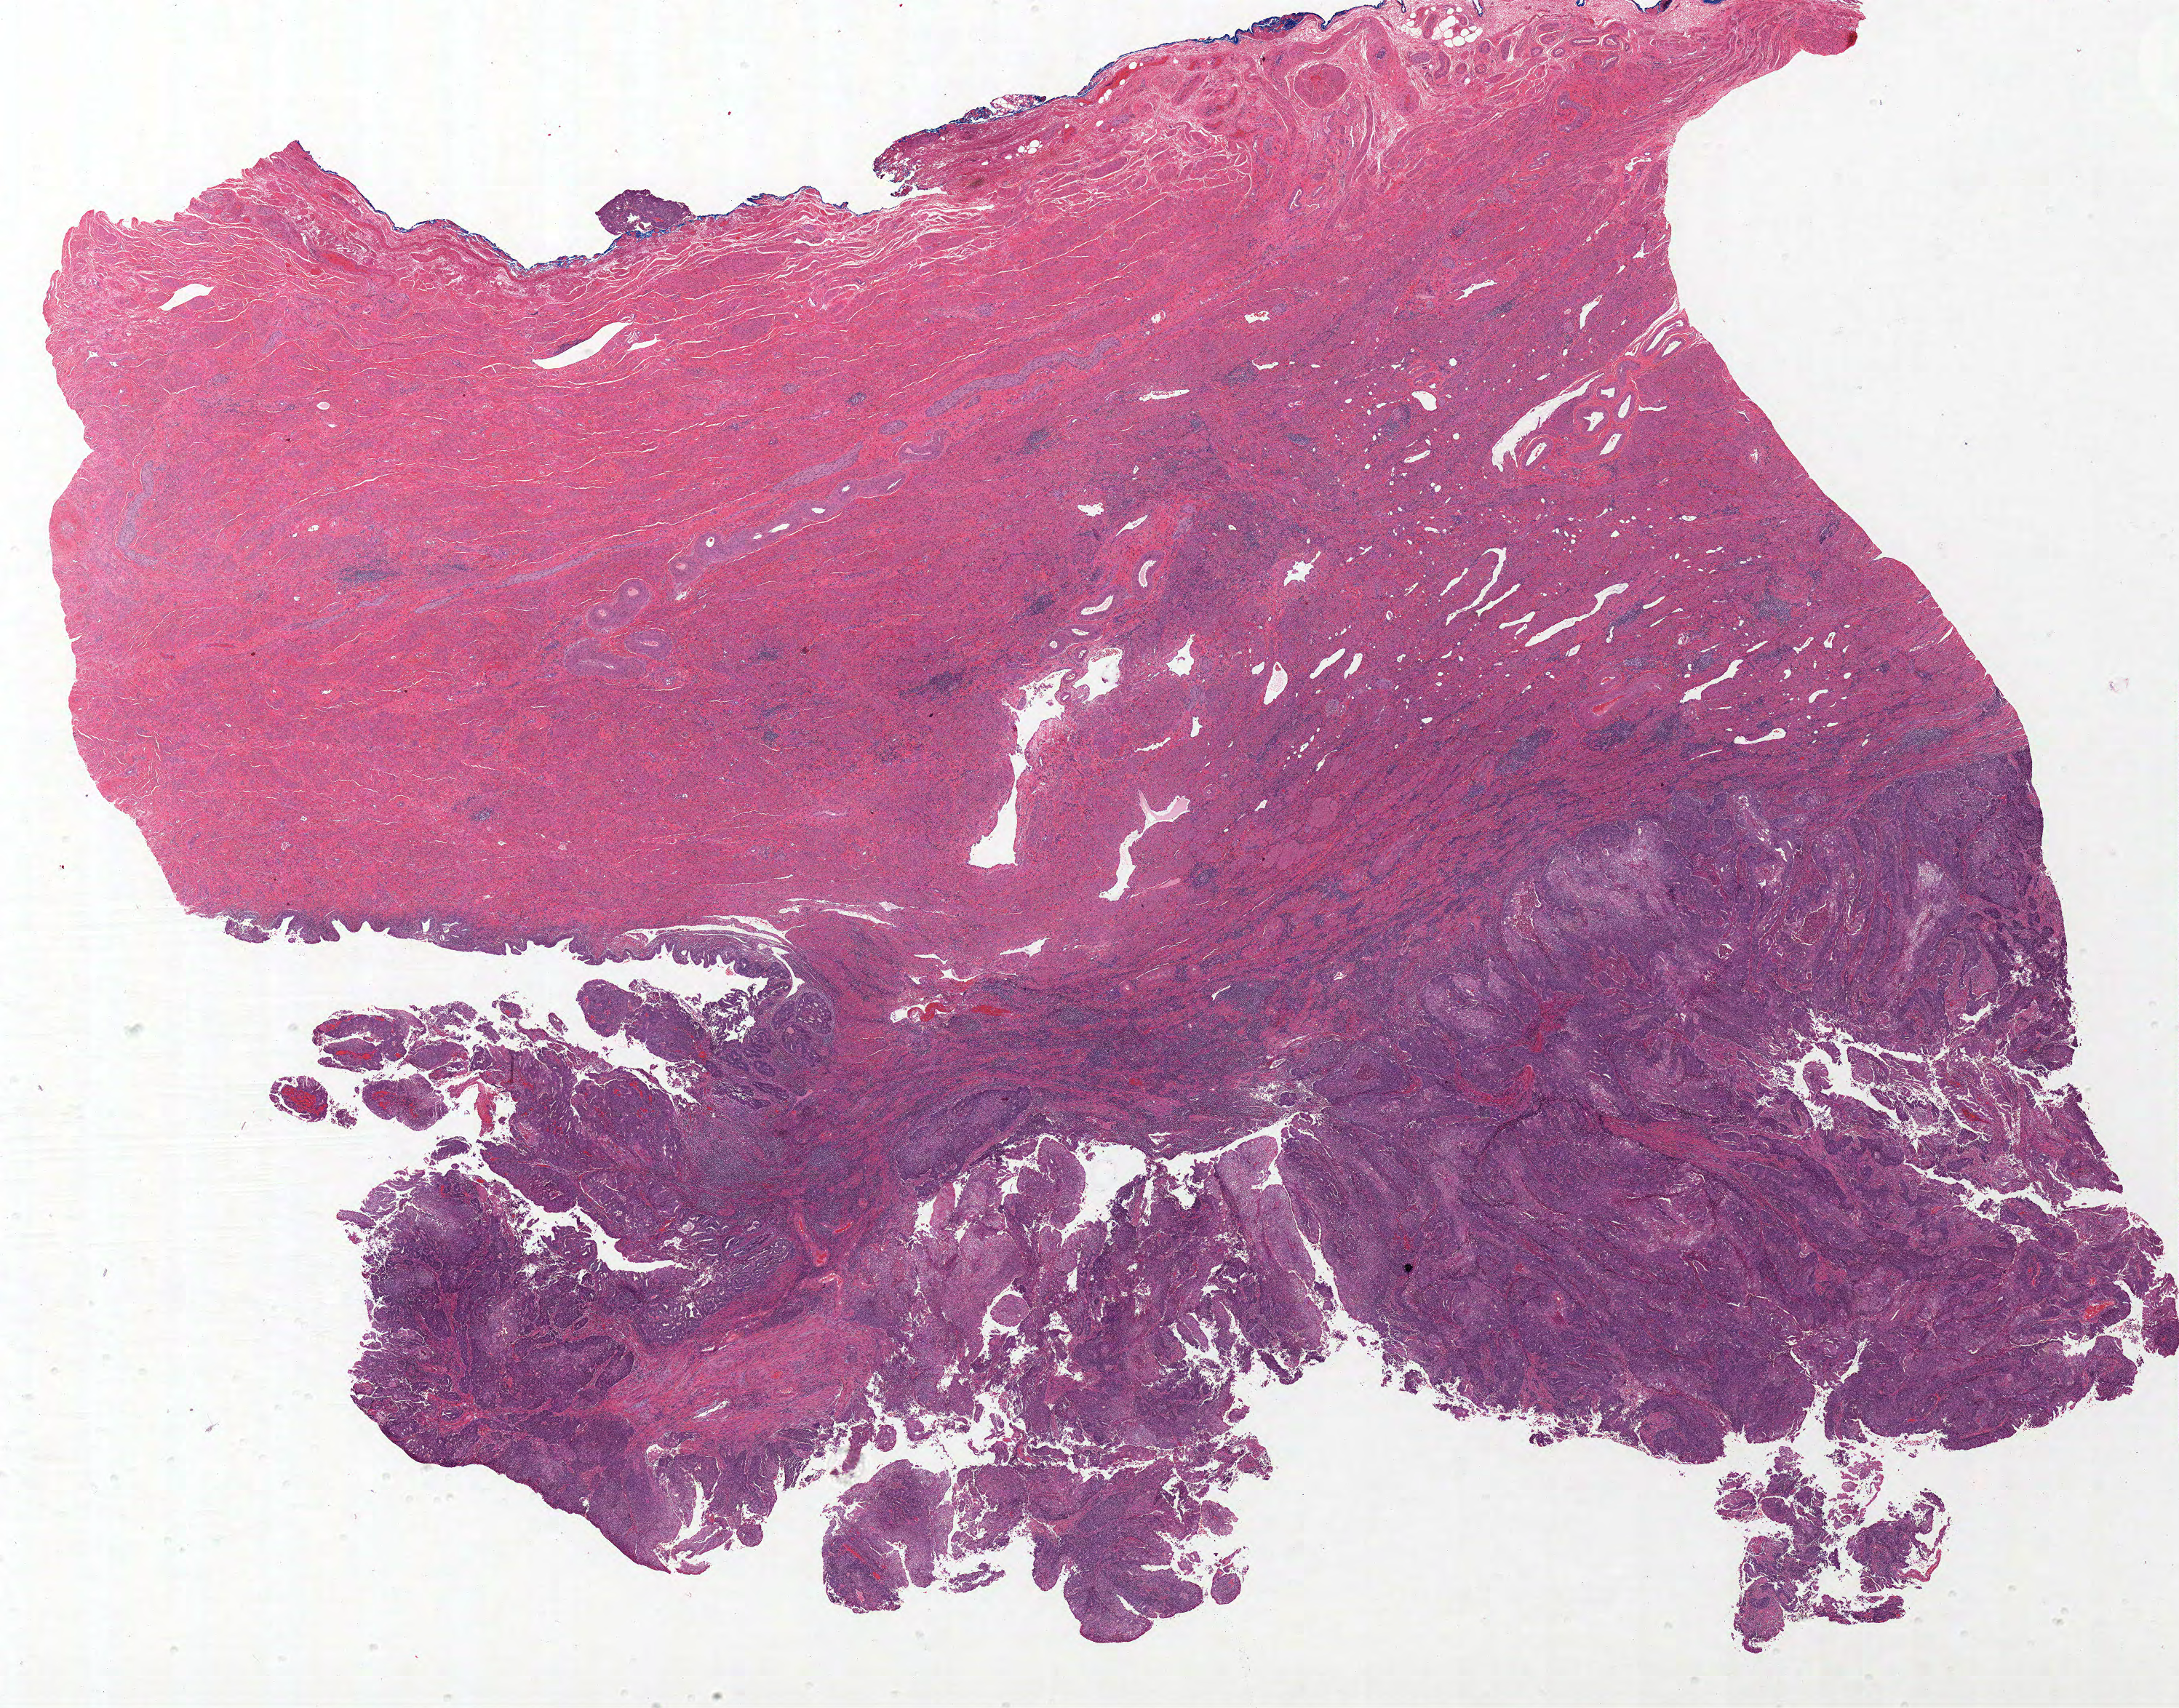
H&E whole-slide image, a low-resolution overview of the entire scanned area, about 23.9 x 18.7 mm (slide scanned at 20x), formalin-fixed paraffin-embedded (FFPE) diagnostic section, uterus, primary tumour sample. Patient: female, age at initial diagnosis 59 years. Histologic grade: G2 (moderately differentiated).
Diagnosis: Endometrioid adenocarcinoma, NOS (endometrium). FIGO stage: IIIC1.